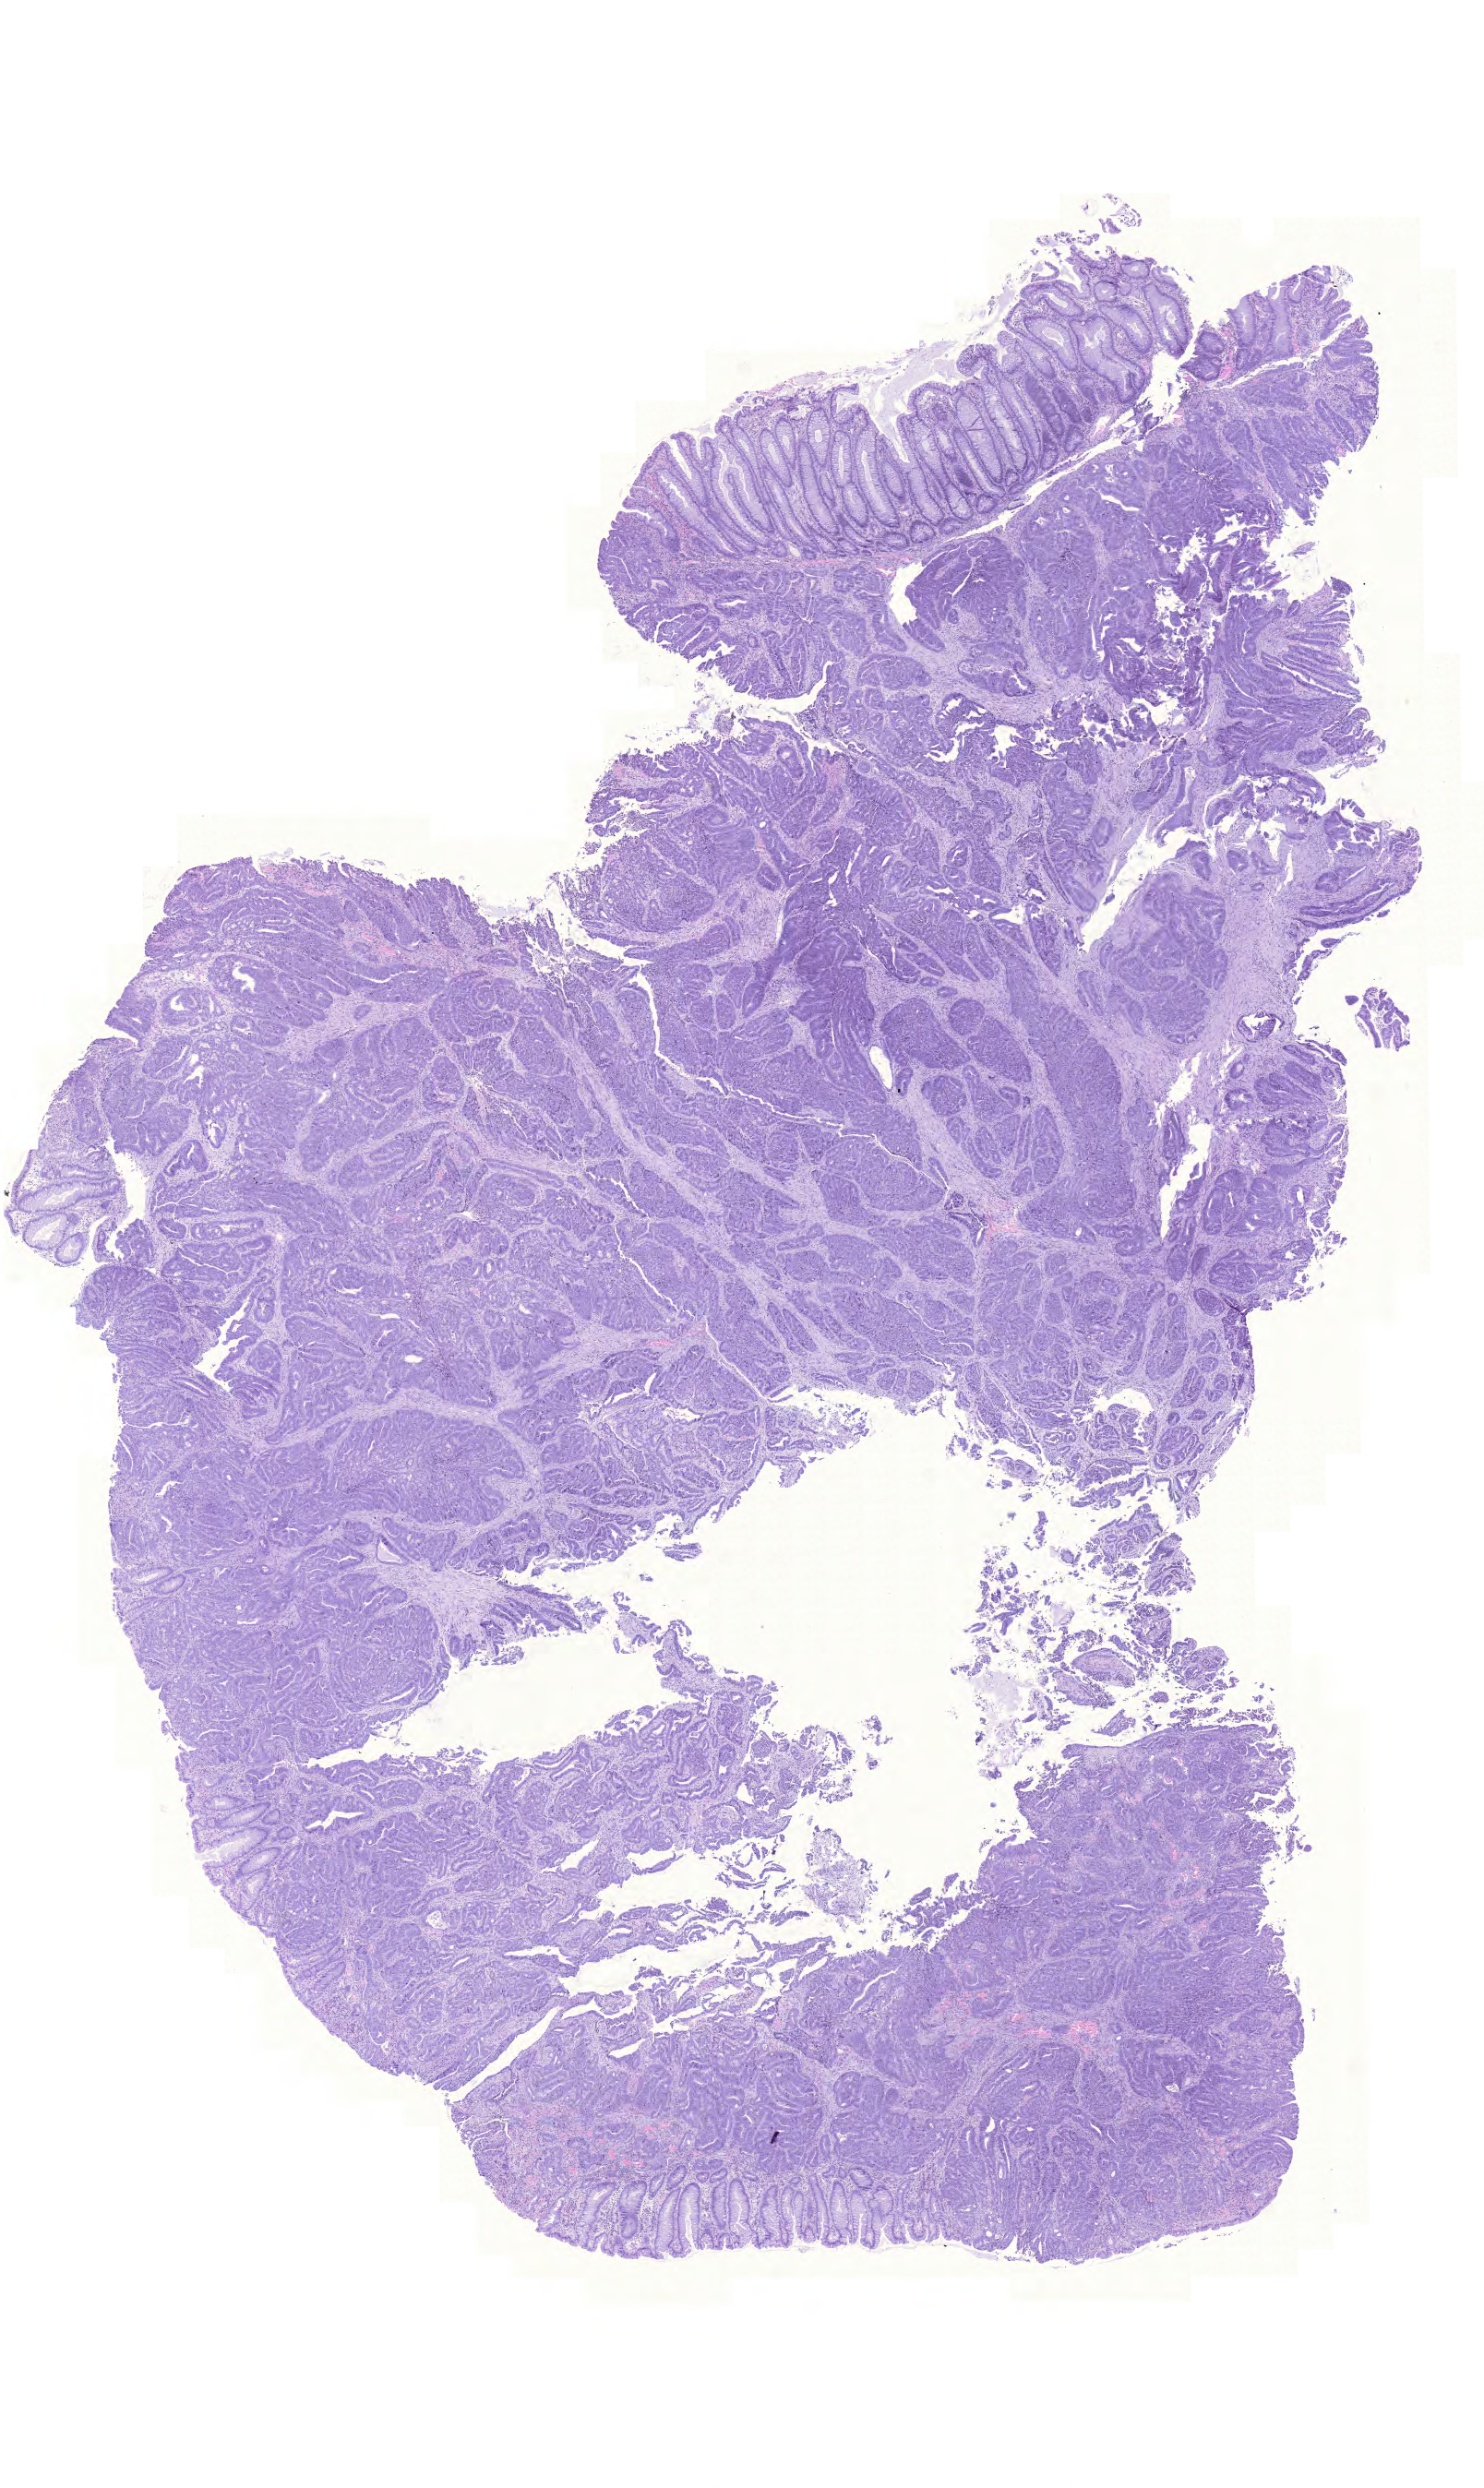
Hematoxylin and eosin (H&E) stained whole-slide image, a low-resolution overview of the entire scanned area, about 12.0 x 20.1 mm; formalin-fixed paraffin-embedded (FFPE) diagnostic section; sample: primary tumour, colon. Female patient; age at initial diagnosis 78 years.
Histologic diagnosis: Adenocarcinoma, NOS (sigmoid colon). AJCC pathologic stage: IIIC (6th edition).